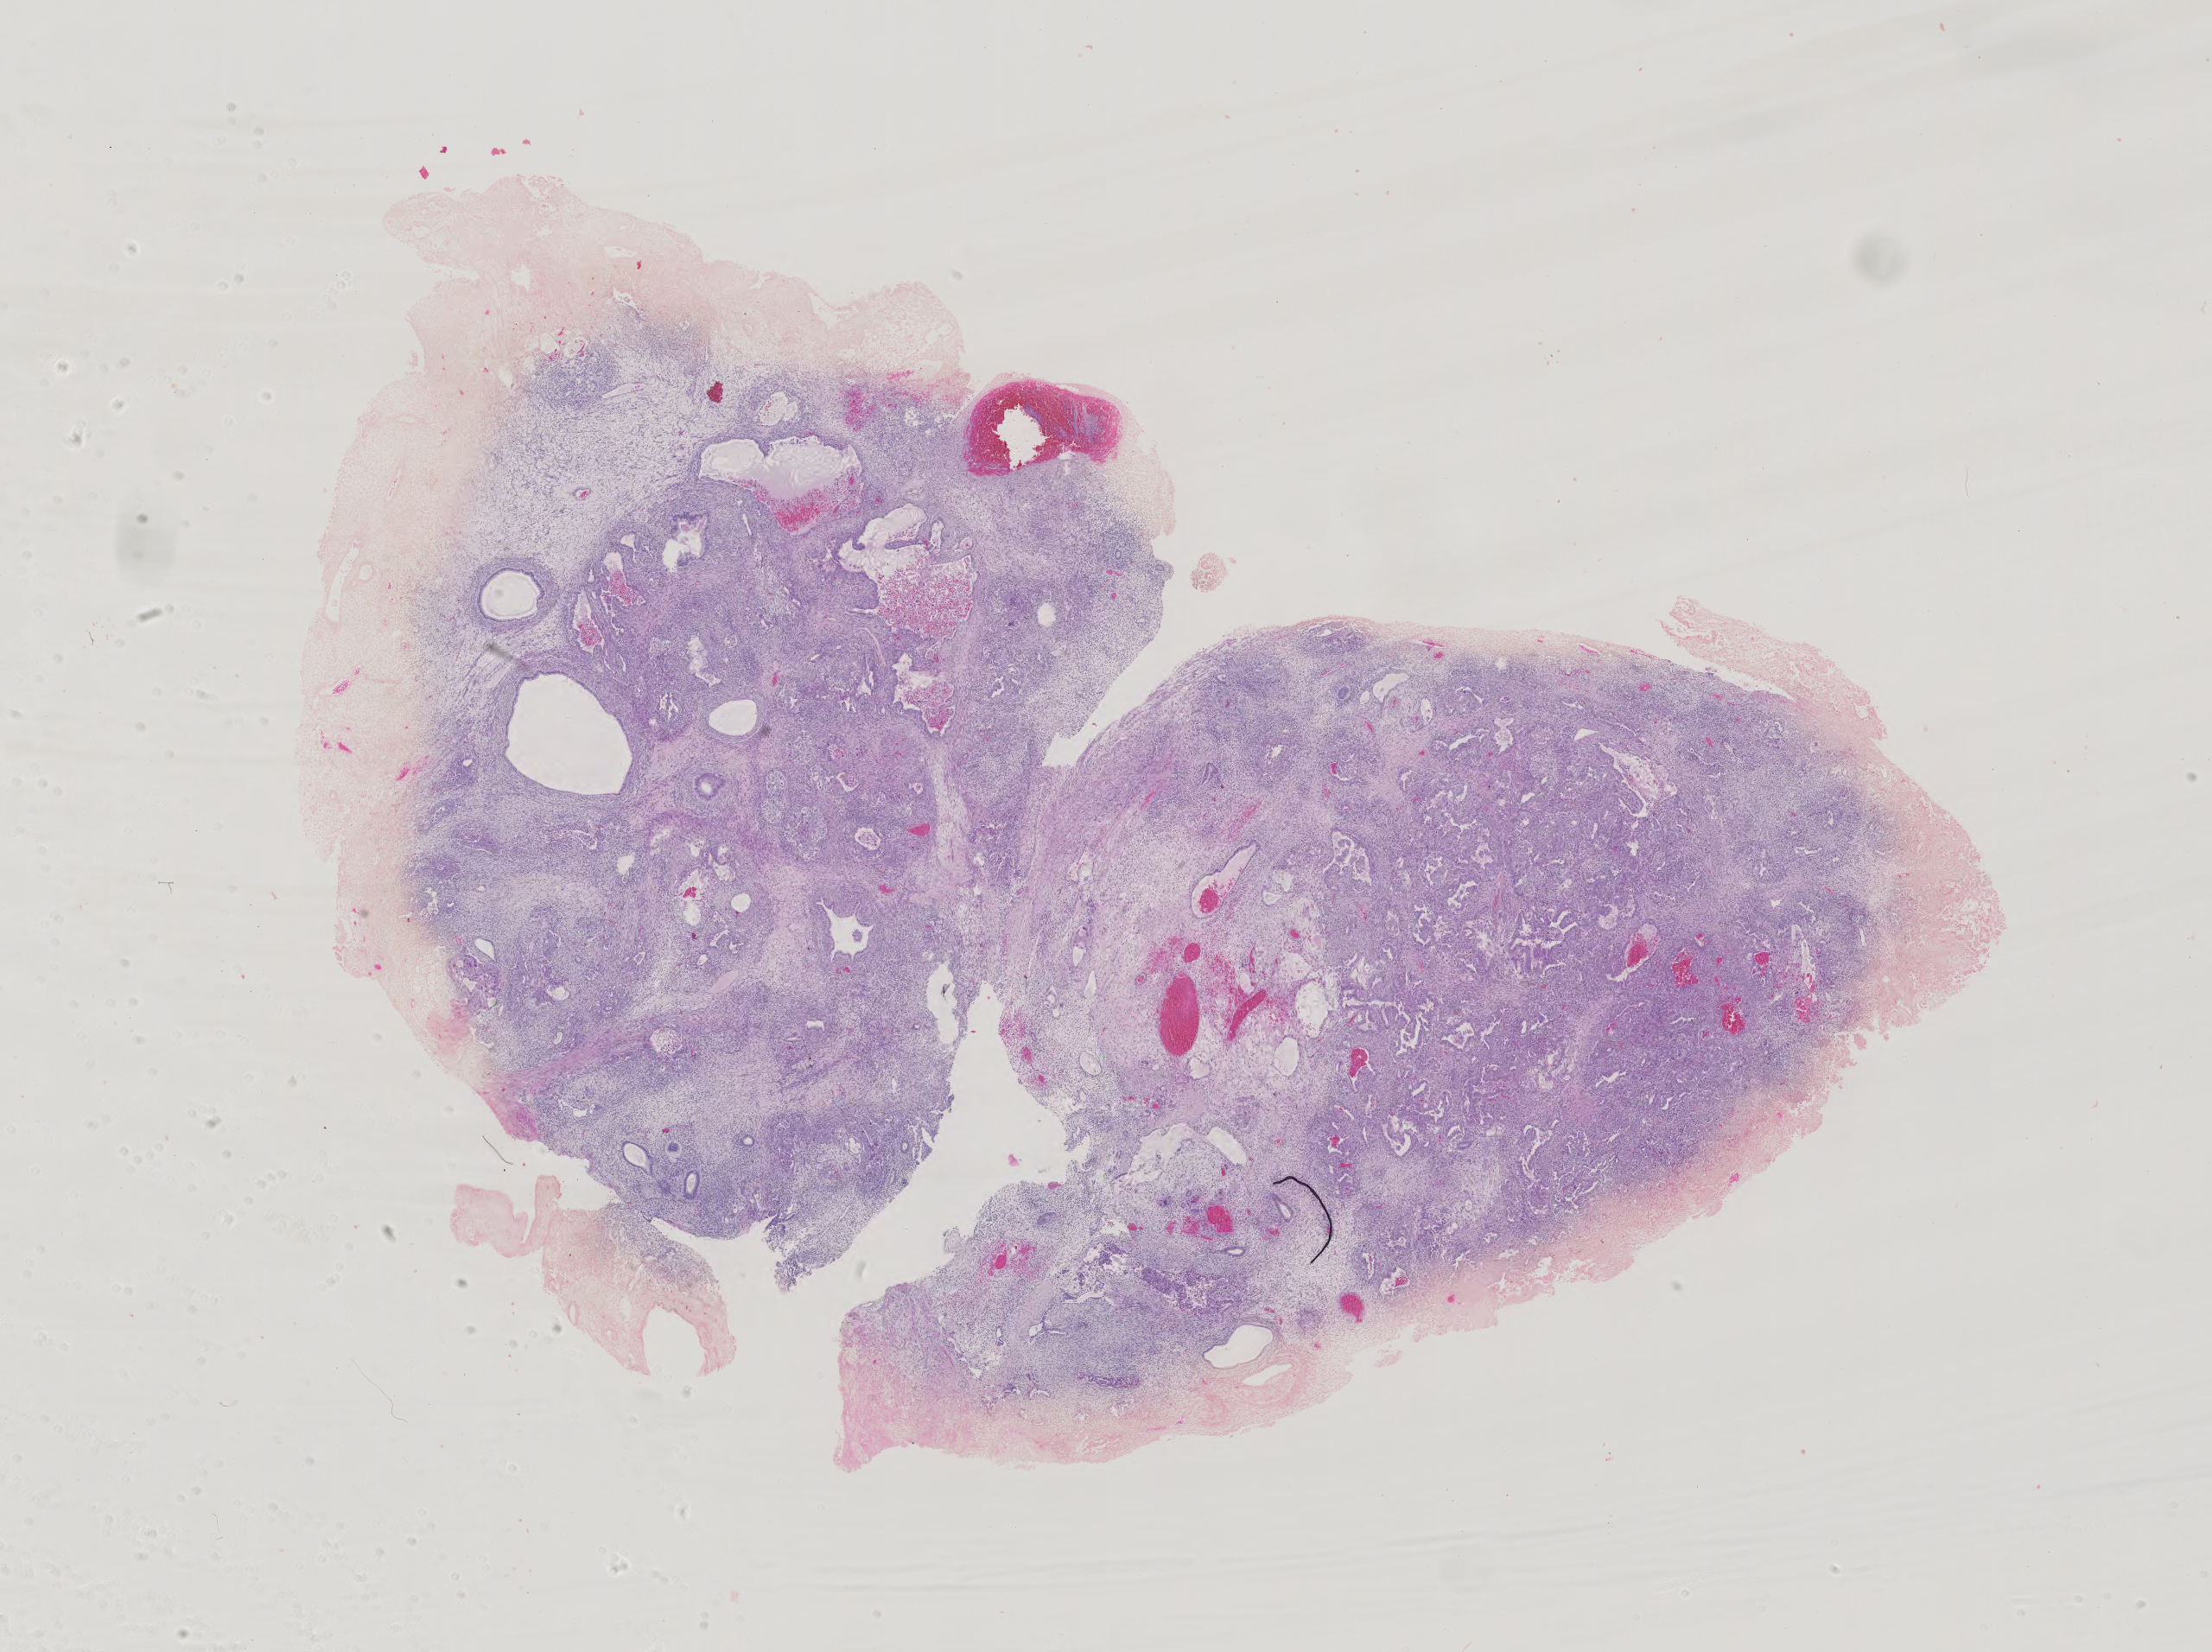
H&E whole-slide image — whole scanned area (about 18.7 x 13.9 mm) shown as a low-resolution overview, formalin-fixed paraffin-embedded (FFPE) diagnostic section, testis, primary tumour sample. Male, age 22 years at initial diagnosis.
Histologic diagnosis: Embryonal carcinoma, NOS. Laterality: left. AJCC pathologic stage: I (4th edition).